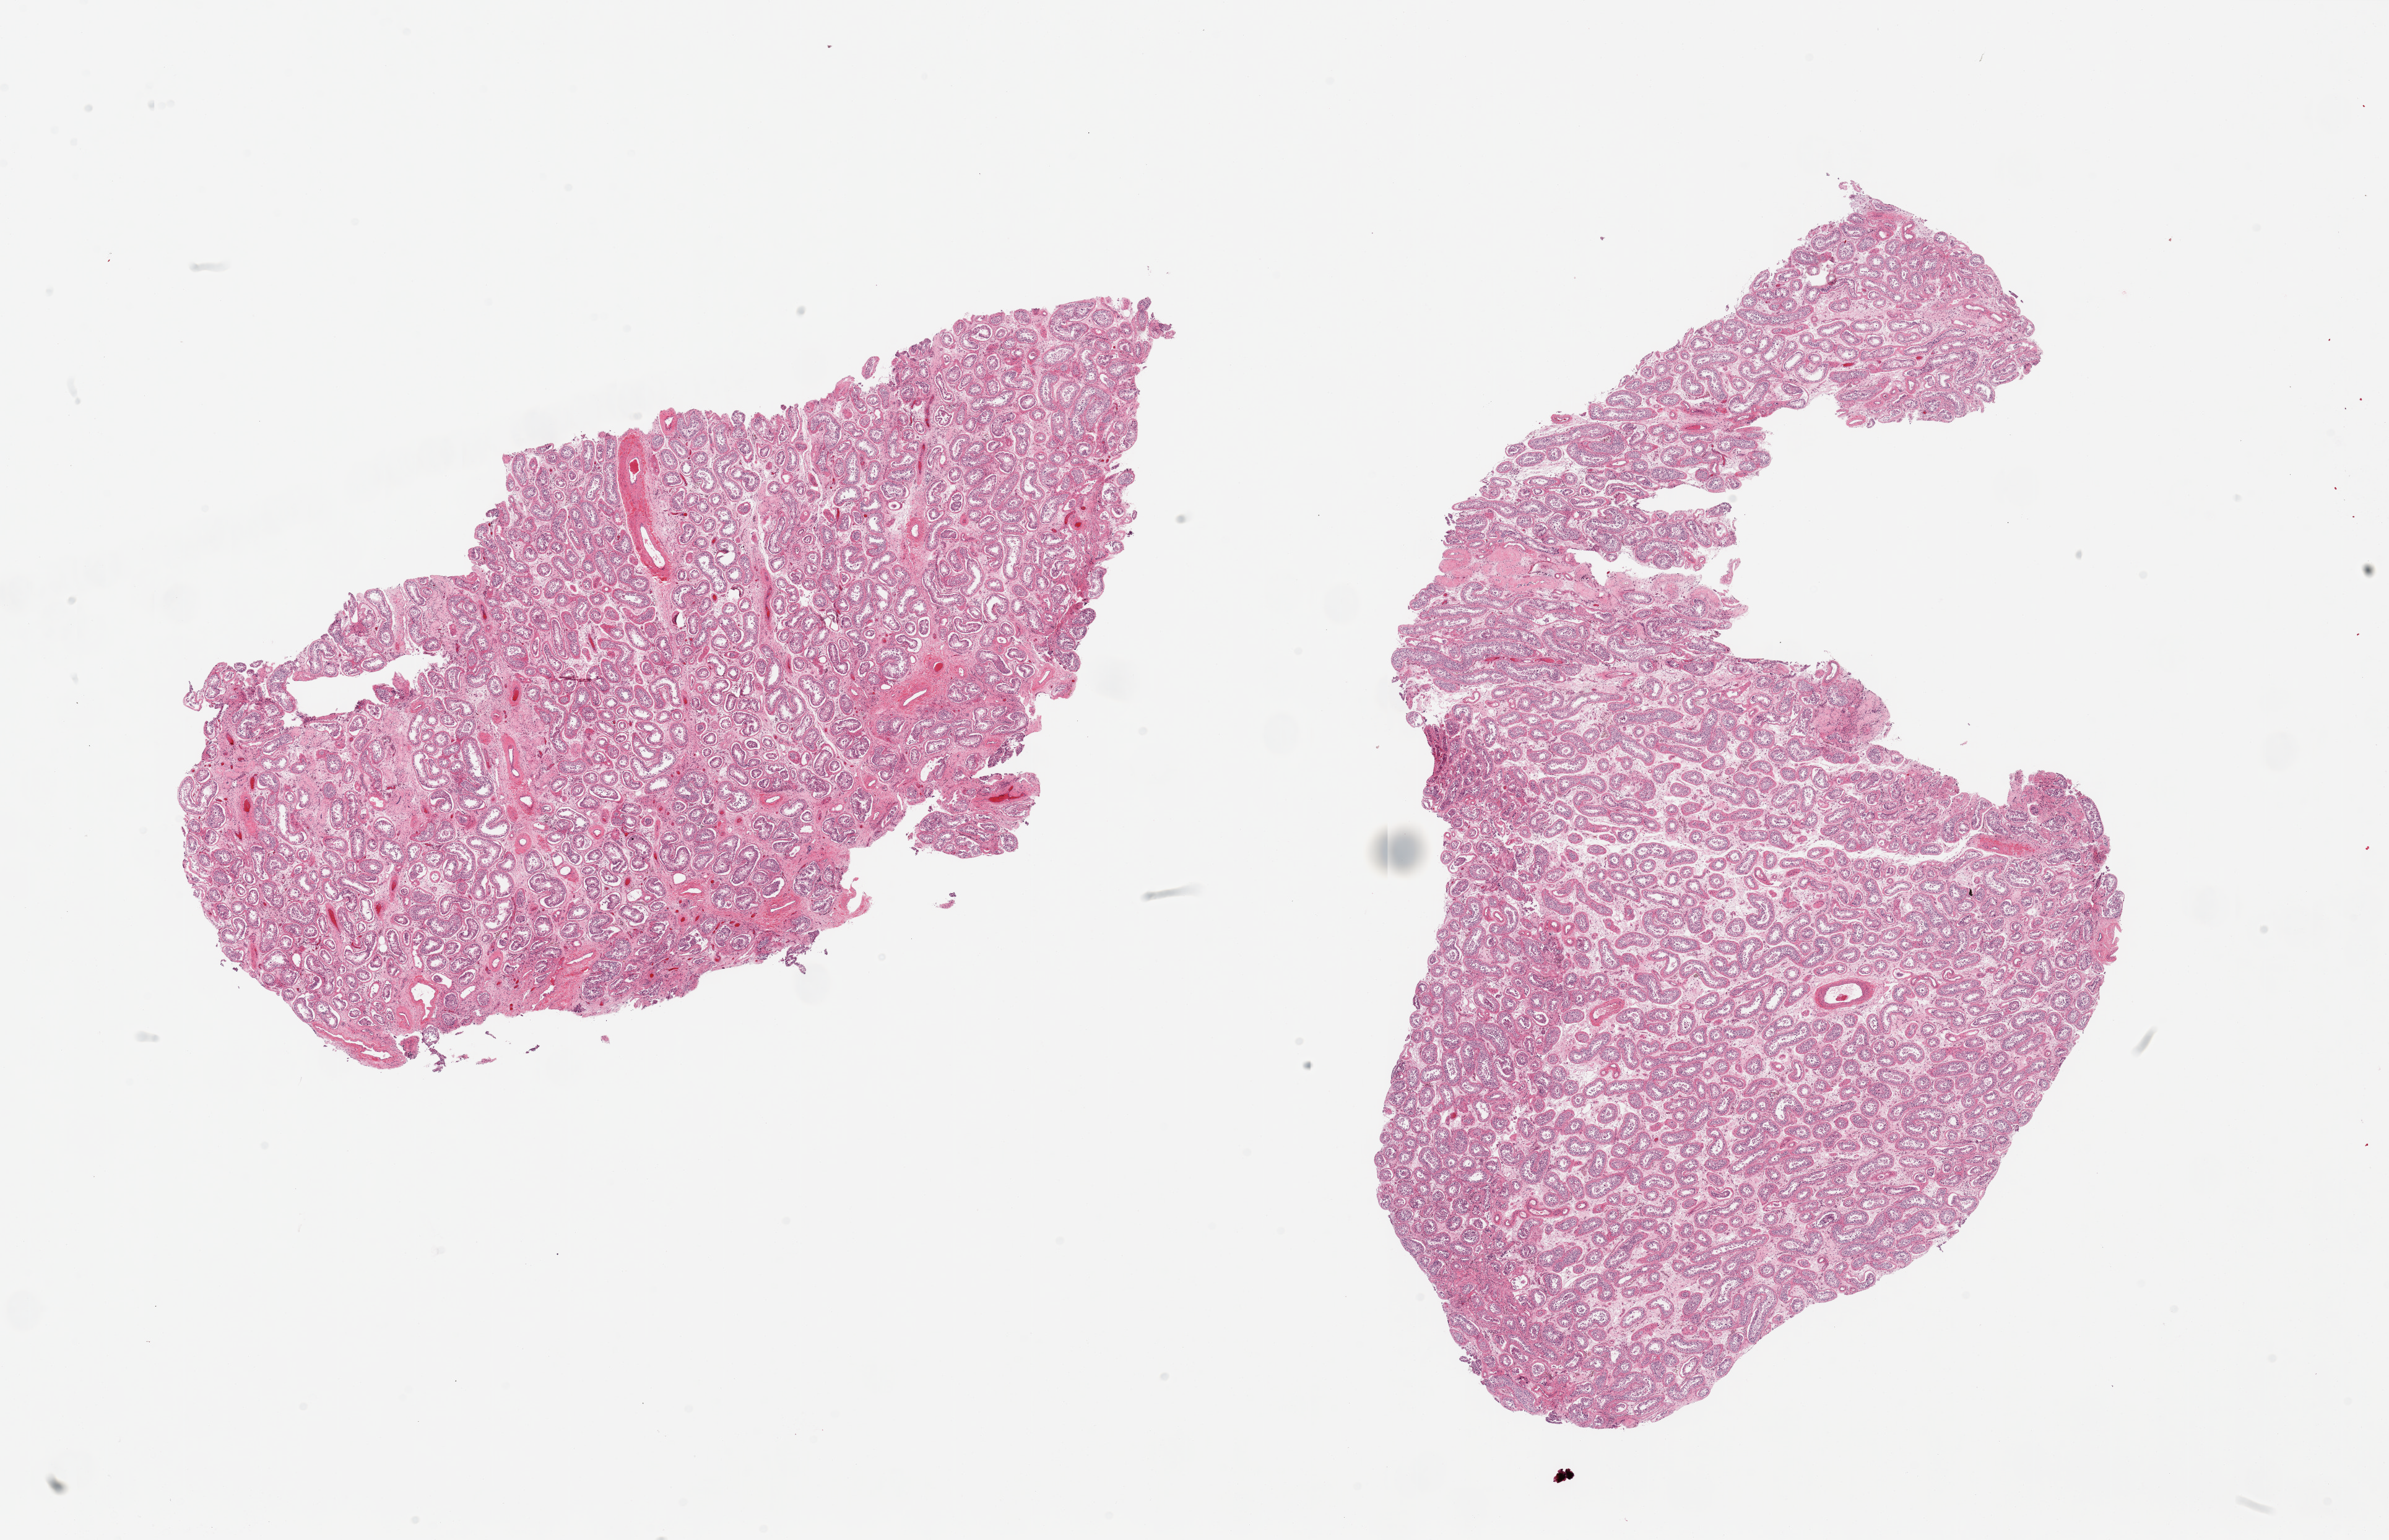
Hematoxylin and eosin (H&E) whole-slide image — whole scanned area (about 30.5 x 19.7 mm) shown as a low-resolution overview; PAXgene-fixed paraffin-embedded (PFPE) section; sampled site (target tissue): testis; tissue donor sample. Donor: male.
• review note (as recorded): 2 pieces, spermatogenesis is reduced